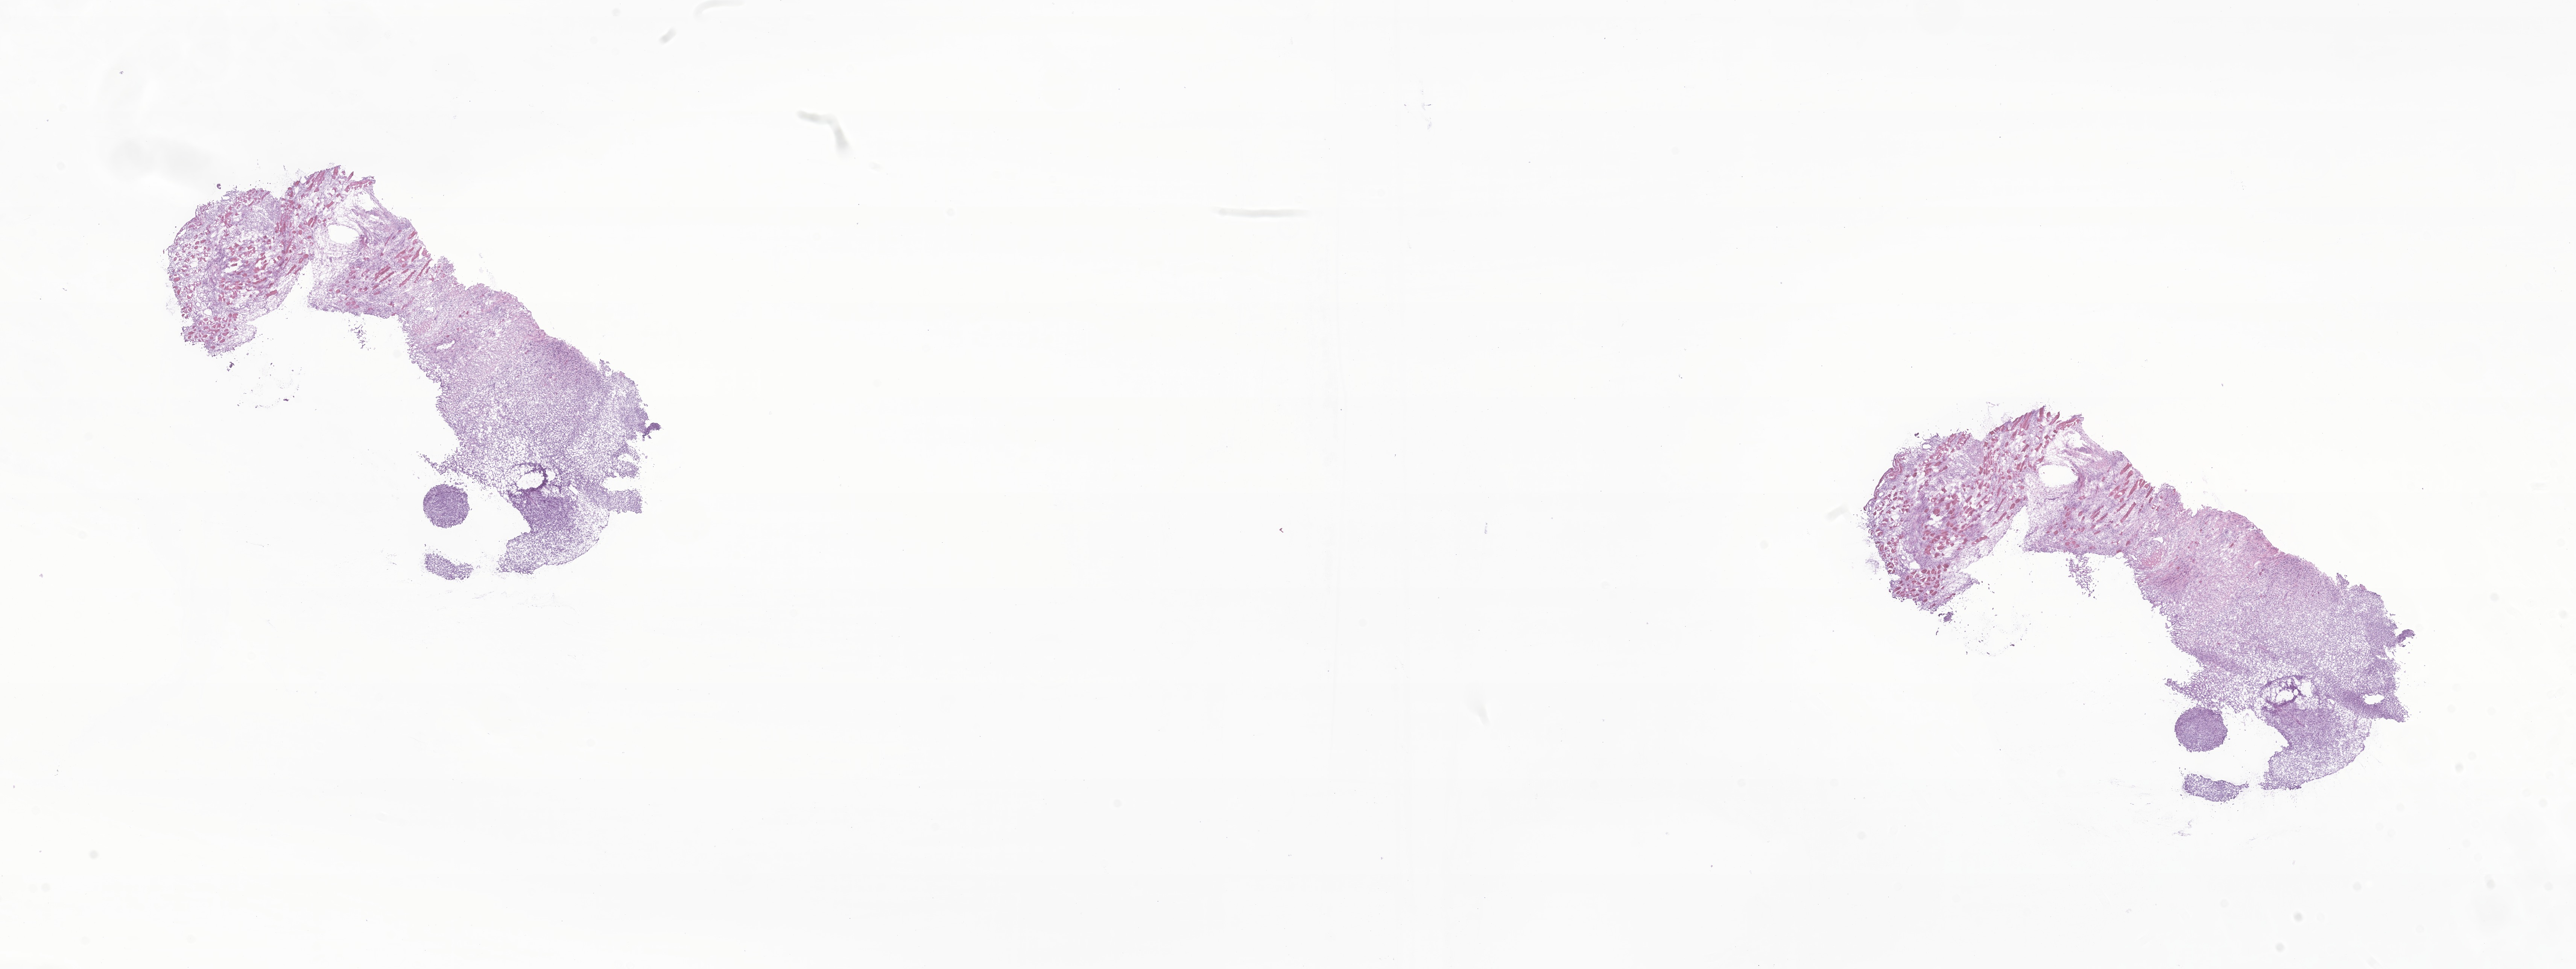
Digitized hematoxylin and eosin (H&E)-stained section of tumor tissue from the soft tissue, low-resolution overview of the scanned area, about 28.9 x 10.9 mm. Cryosection (OCT / tissue freezing medium). Patient: male, age 134 days.
• diagnosis (ICD-O-3 morphology term): Infantile fibrosarcoma